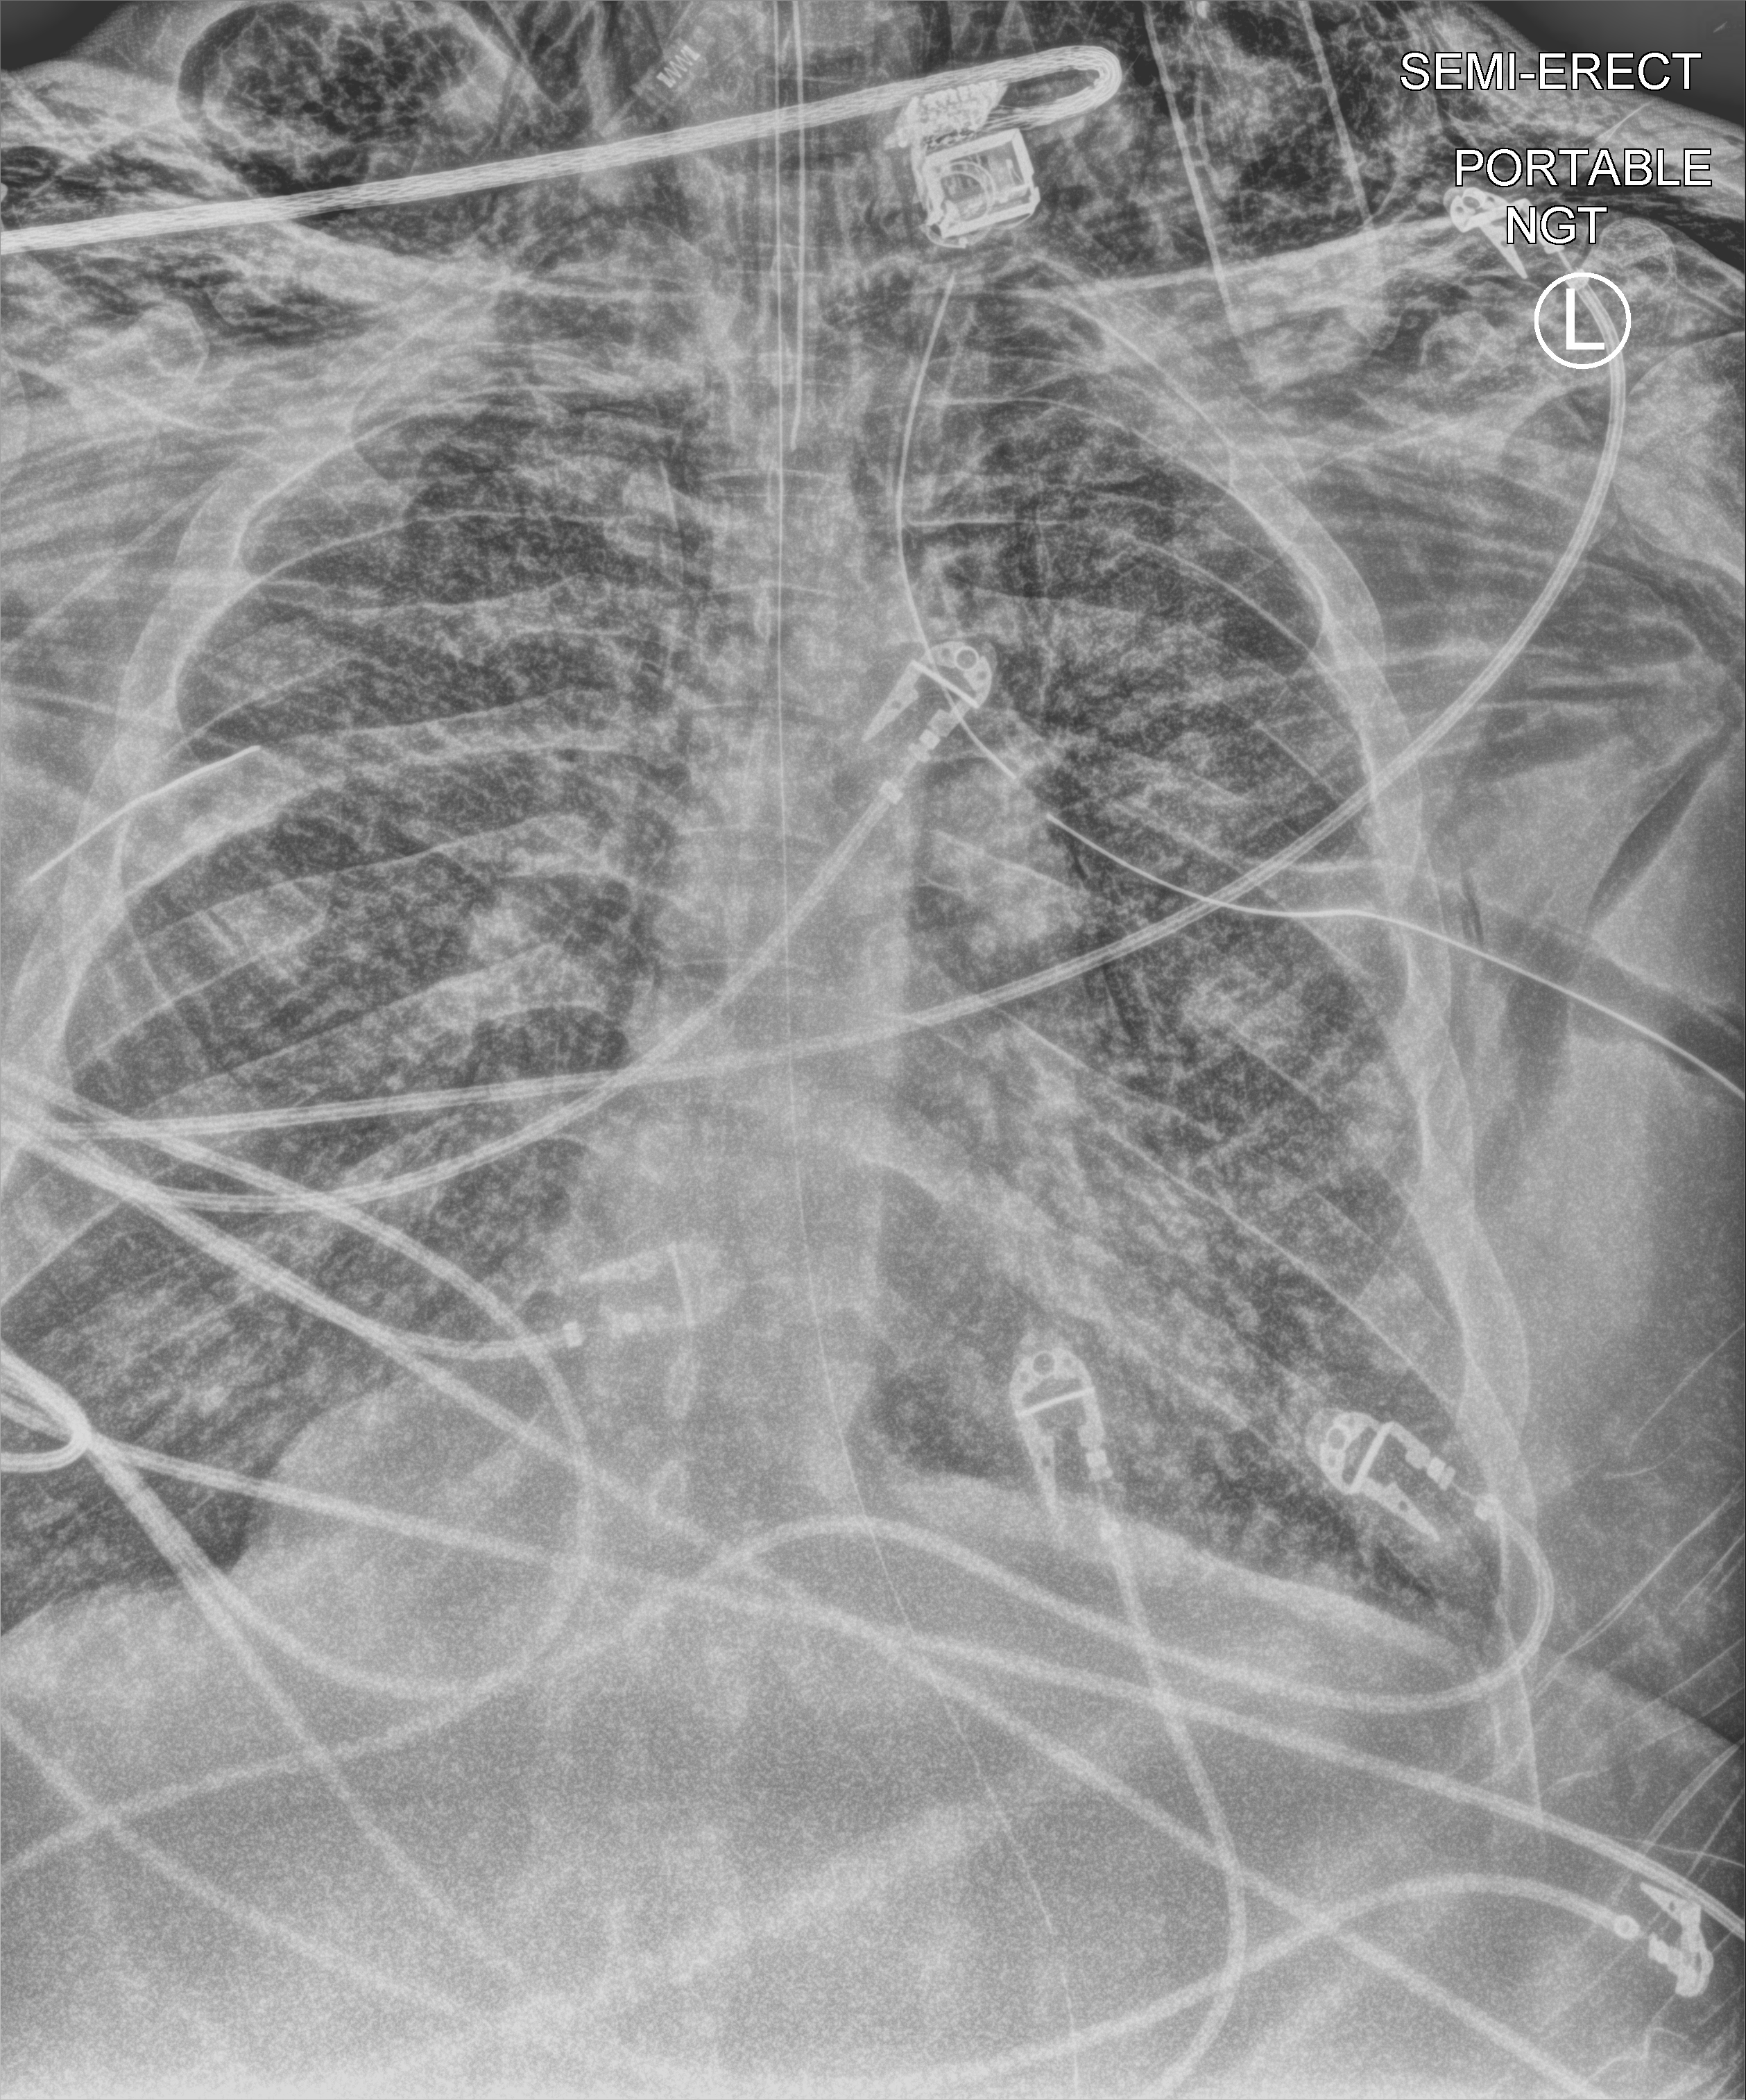
Portable chest radiograph. Patient hospitalised with COVID-19, aged 18–59 years.
Admission-level facts for this patient (not findings on this image; timing relative to this image not recorded):
- hypertension (admission record): no
- mechanically ventilated during this hospital stay: yes
- admitted to intensive care during this hospital stay: yes